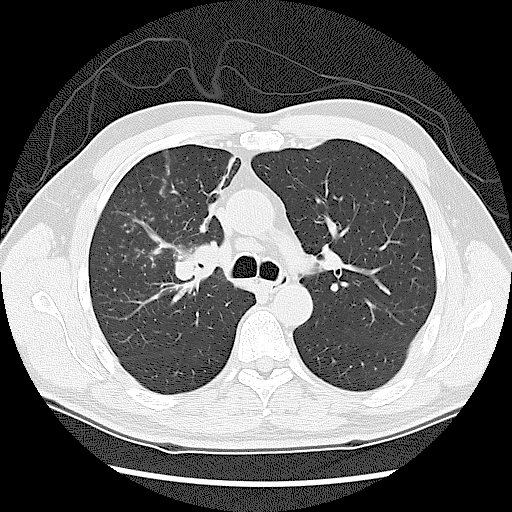
Chest CT (low-dose screening protocol), one axial image; baseline screening round; lung window (W 1500 / L -600 HU); 2.5 mm slice thickness; lung (sharp) reconstruction kernel (LUNG); slice 48 of 131 in the series; 512 × 512 image matrix, field of view 360 × 360 mm. Male participant, aged 60 years at enrolment.
Lesion marked by an expert reader, box from (x=159, y=222) to (x=244, y=317) px. No non-calcified nodule or mass ≥4 mm was recorded by the screening reader at this exam. Participant outcome: lung cancer diagnosed 41 days after this screen — small cell carcinoma, NOS, right upper lobe, stage IIIA (AJCC 6th edition).